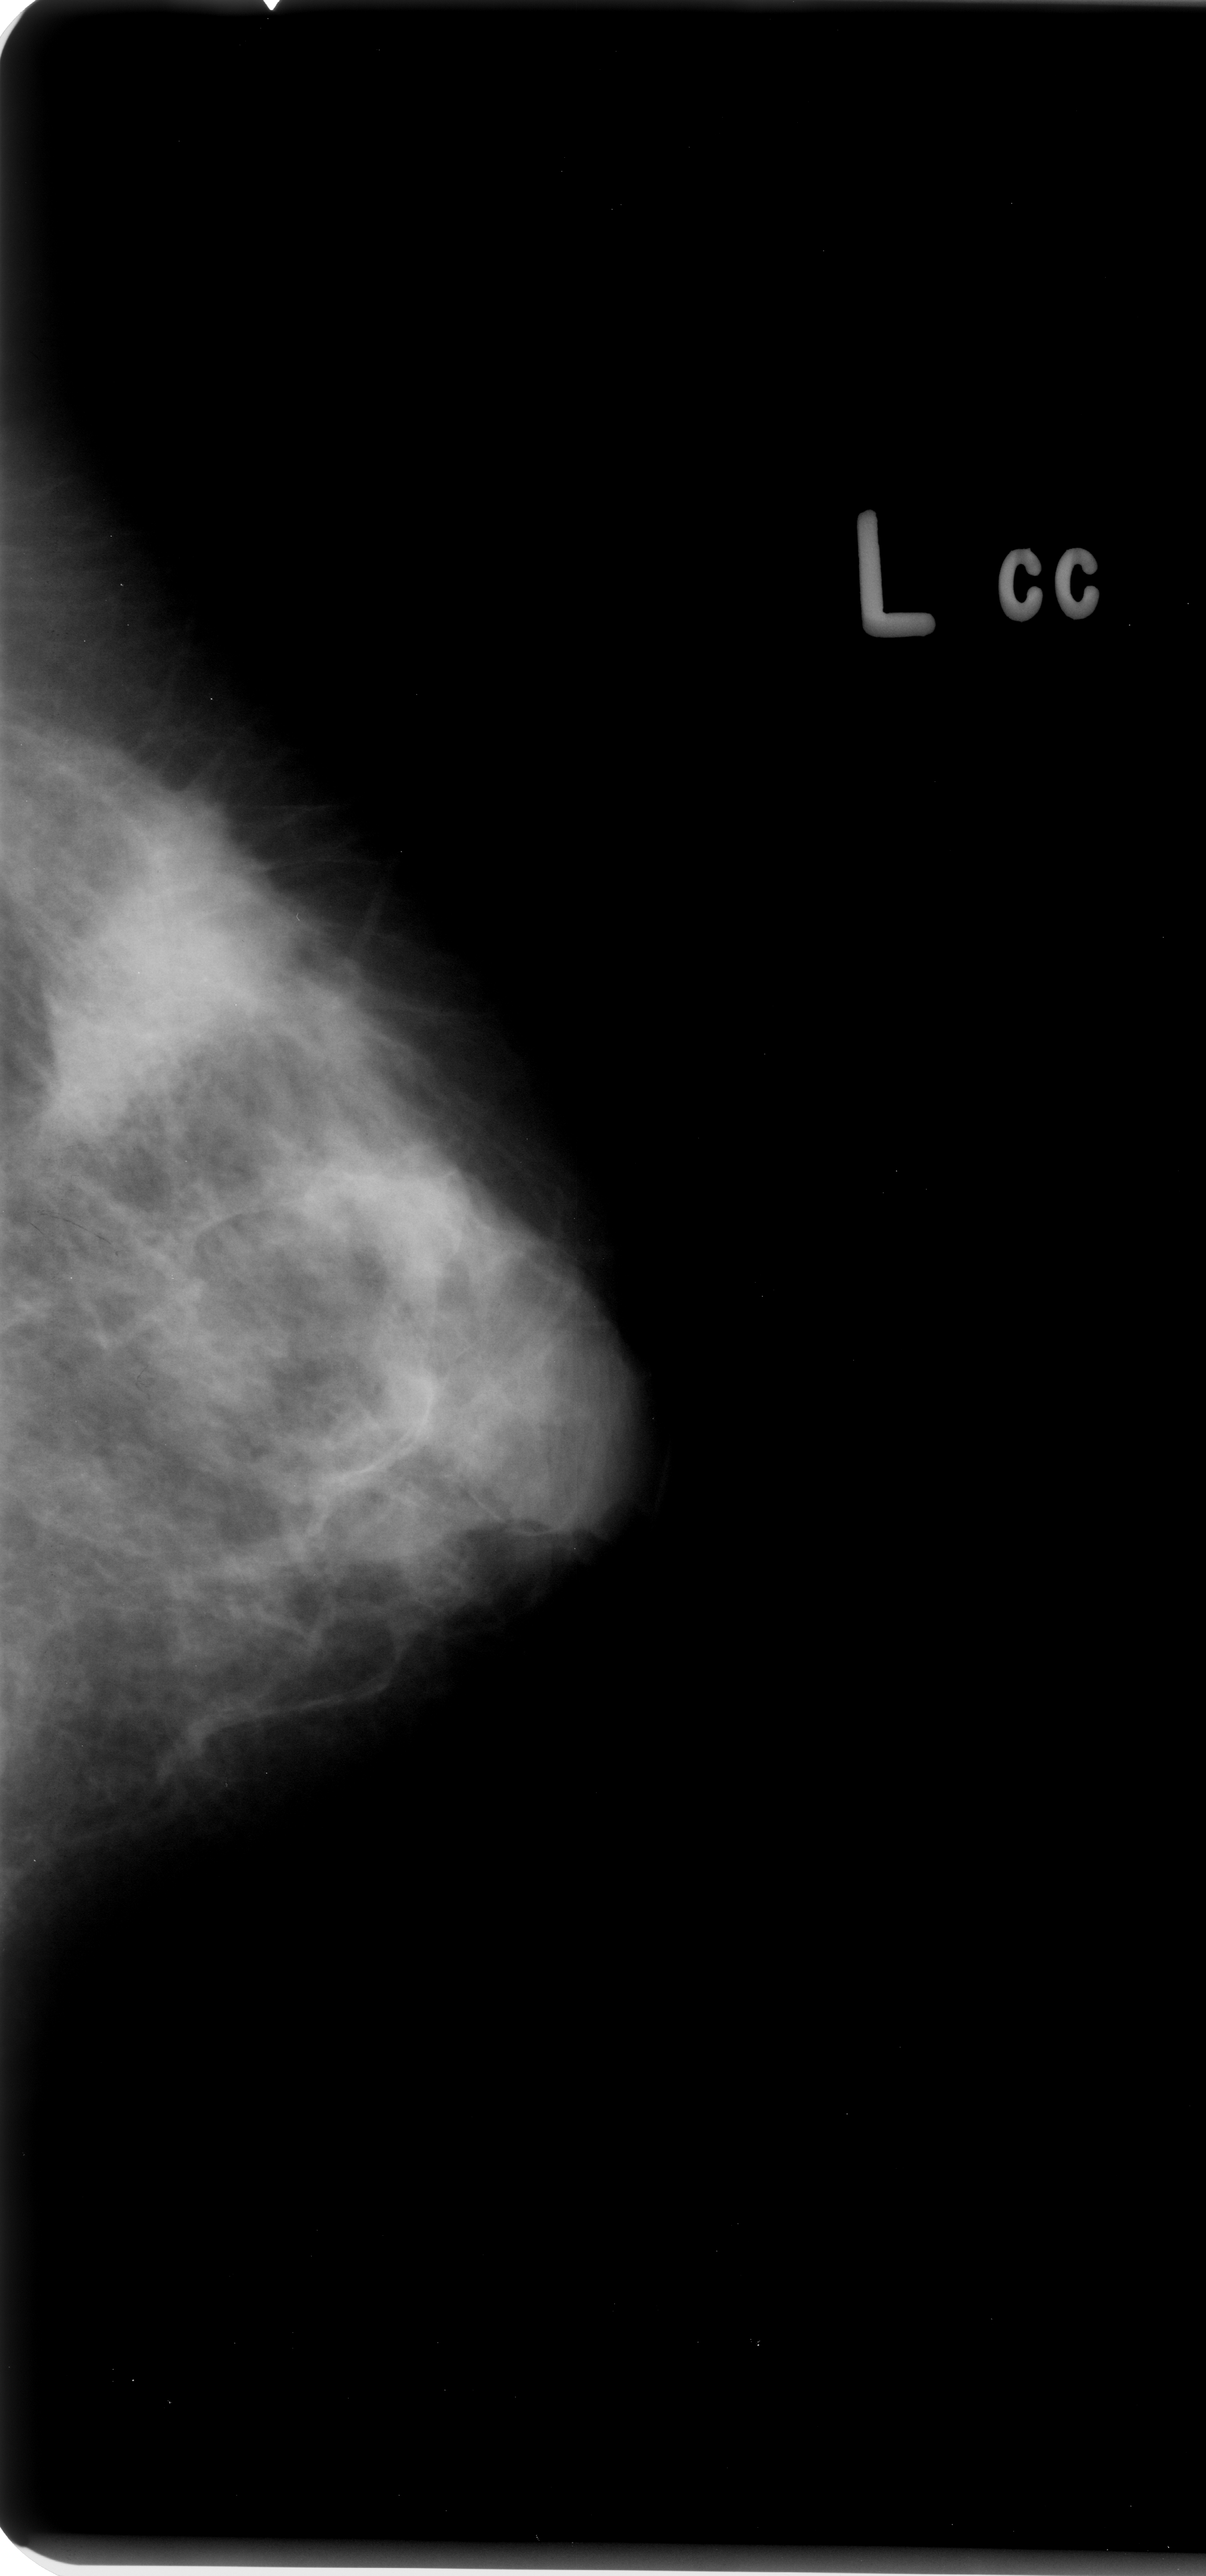
Scanned film-screen mammogram; left breast; CC view.
Abnormality record for this image: mass, shape irregular / architectural distortion, margins obscured / spiculated; BI-RADS assessment category 4; pathology result (as recorded, not read from the image): malignant.